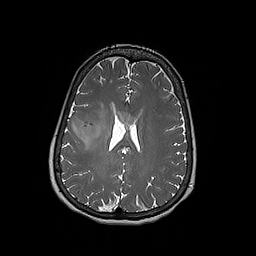
Brain MRI from a brain-tumour surgery series, one axial slice; position 79 of 192 along the scan axis; 1 mm slice thickness; 256 × 256 image matrix. Case-level facts recorded for this patient, not image findings: histopathology: Oligodendroglioma; WHO grade: 3; IDH mutation: yes; tumour location: Right Frontal.
Outlined on this slice (manually delineated by an expert):
- tumour: bounding box [x1, y1, x2, y2] px = [72, 115, 102, 141]